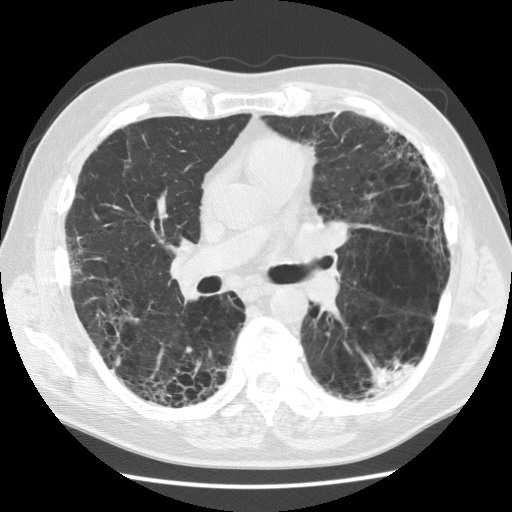
Low-dose screening chest CT, one axial slice. 120 kVp. Lung window (W 1500 / L -600 HU). 2.5 mm slice thickness. 512 × 512 image matrix, field of view 360 × 360 mm.
Structures marked on this image (outlined manually by an expert reader):
- lesion 1 (tumor, lower lobe of left lung): bounding box <371,363,415,392> (left, top, right, bottom; pixels)